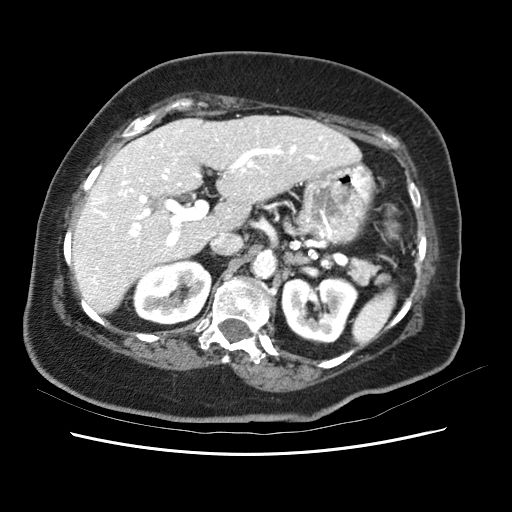
Contrast-enhanced abdominal CT (liver protocol), one axial slice. Position 35 of 62 along the scan axis. Soft-tissue window (W 400 / L 40 HU). 2.5 mm slice thickness. 512 × 512 image matrix, field of view 340 × 340 mm. Case-level facts recorded for this patient, not image findings: diagnosis: hepatocellular carcinoma (patient treated with transarterial chemoembolisation; whether this scan precedes or follows treatment is not stated here); TNM stage (as recorded): Stage-I; Child-Pugh class: B; tumour nodularity: uninodular; tumour size: 5.3 cm.
Structures marked on this image (semi-automatically segmented with operator editing):
- liver parenchyma outside the tumour (the mass and vessels are separate outlines, so this box may not span the whole liver): bounding box <72,114,363,315> (left, top, right, bottom; pixels)
- liver vessels: <90,128,349,295>